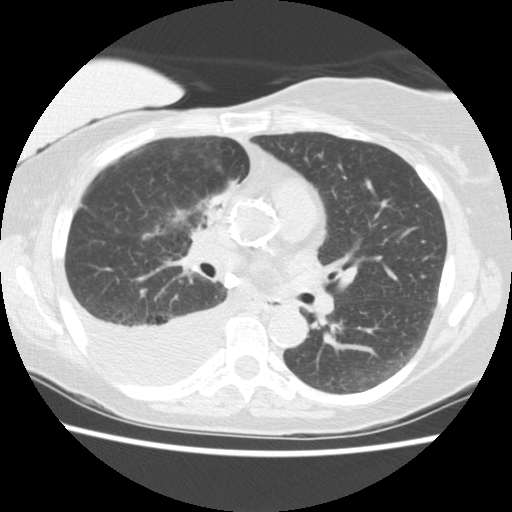
Low-dose screening chest CT, one axial slice. Position 82 of 157 along the scan axis. Reconstruction kernel STANDARD. Lung window (W 1500 / L -600 HU). 2.5 mm slice thickness. 512 × 512 image matrix, field of view 330 × 330 mm.
Outlined on this slice (expert manual segmentation):
- lesion 1 (tumor, upper lobe of right lung): bounding box <205,183,240,220> (left, top, right, bottom; pixels)